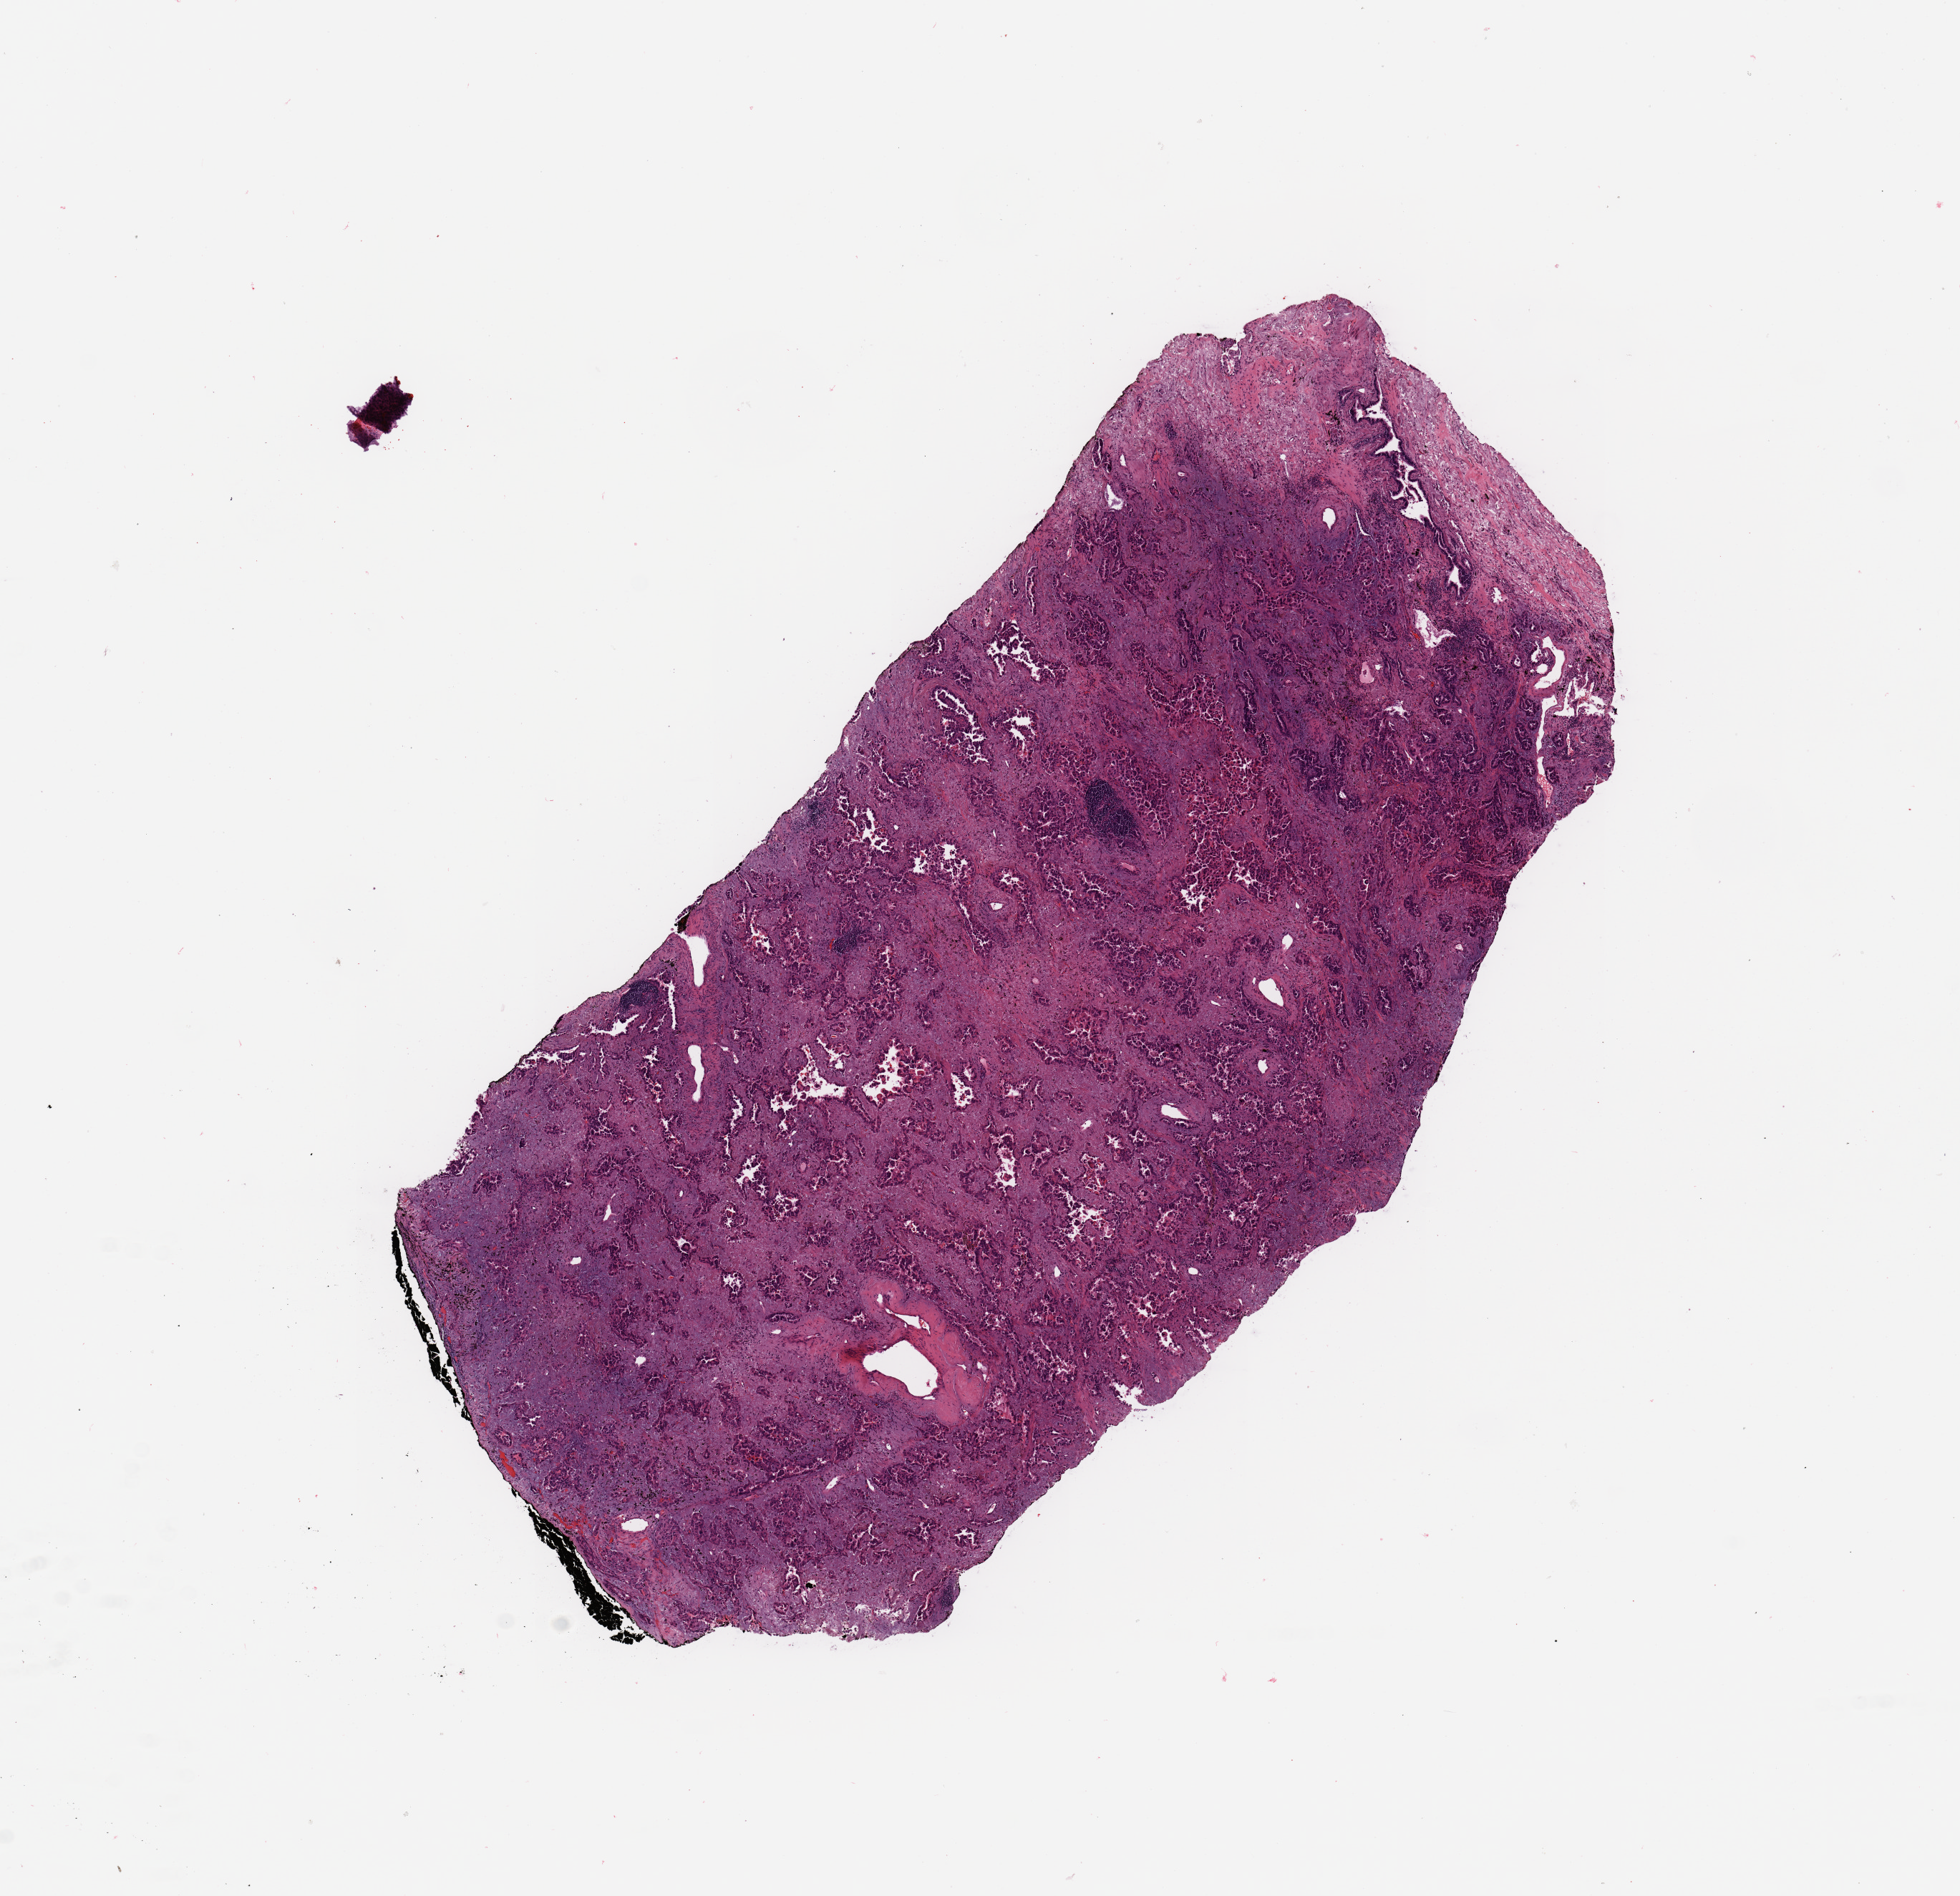
Digitized Hematoxylin and eosin (H&E) stained tissue section (whole slide) — shown as a low-resolution overview of the whole scanned area (about 10.8 x 10.5 mm, slide scanned at 20x). Tumour tissue sample, sampled site: lung. Female, 67 y/o. Histologic grade: G2 (moderately differentiated). Pathologist review of this section (percent, as recorded): tumour nuclei 80%, necrosis 2%.
Primary tumour site (as recorded): left upper lobe. Diagnosis: Adenocarcinoma, NOS. AJCC pathologic stage: IB.